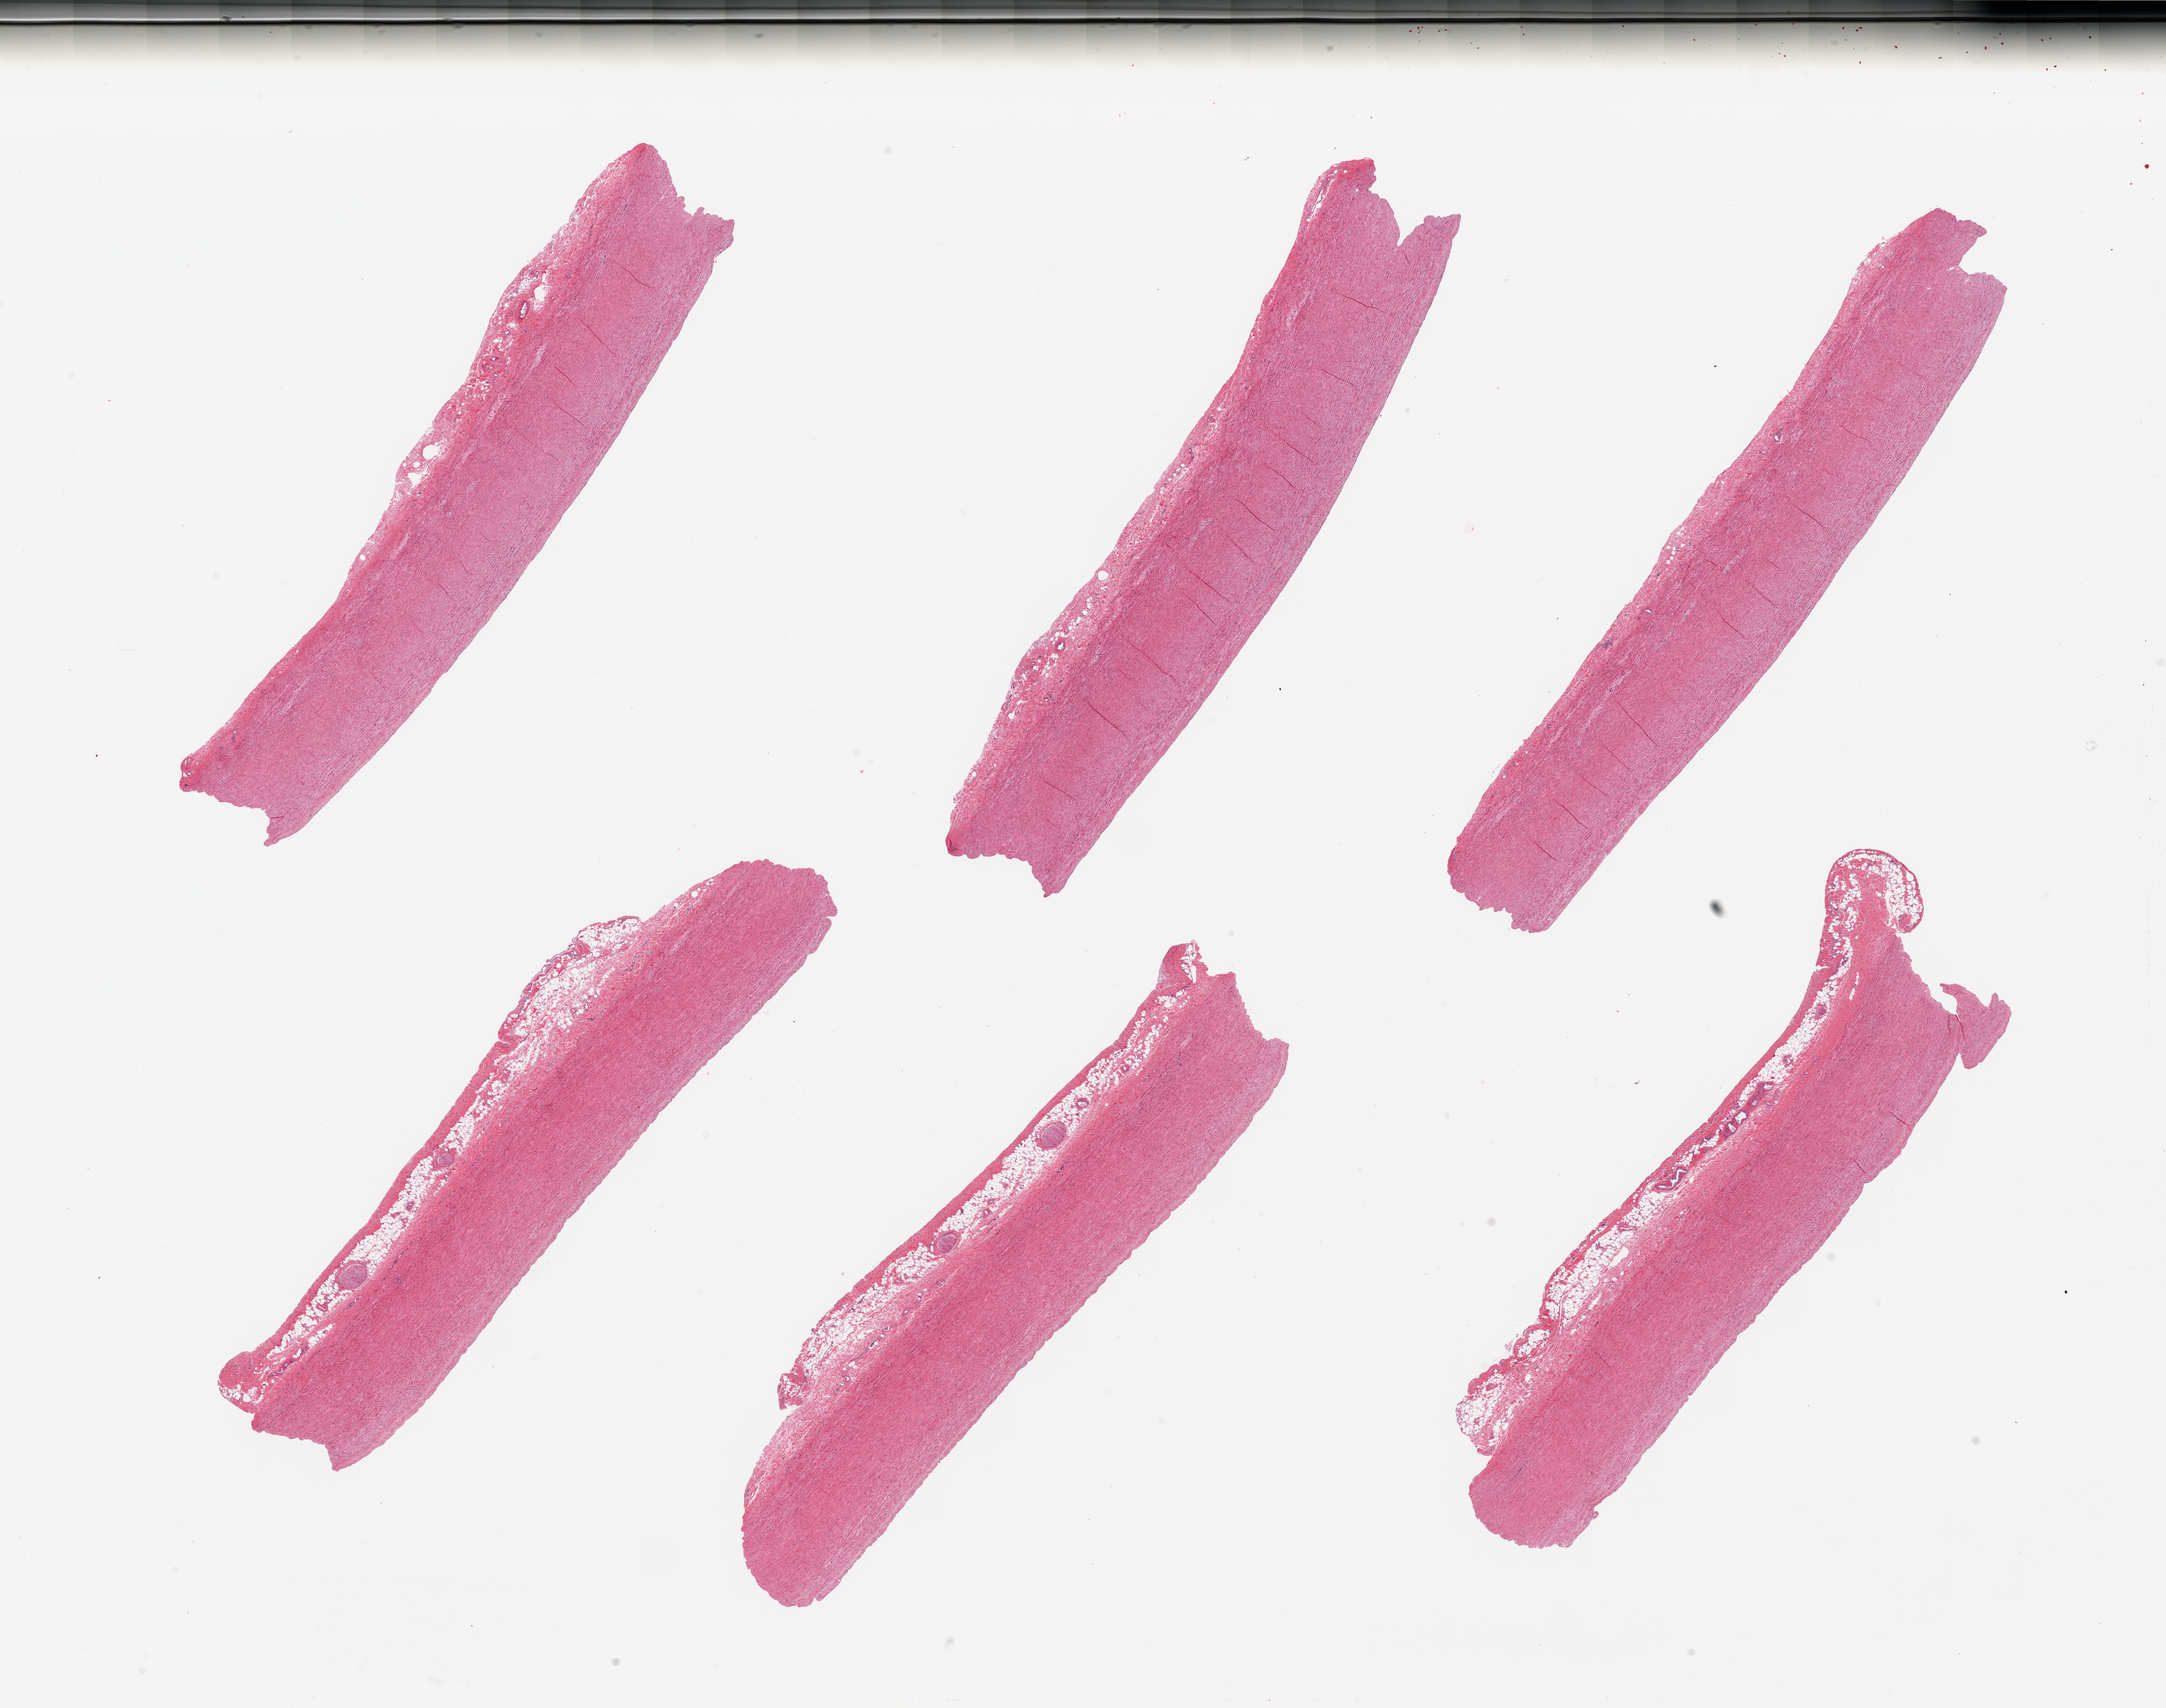
Digitized haematoxylin and eosin-stained section, brightfield, shown as a low-resolution overview of the whole scanned area (about 29.5 x 23.3 mm); PAXgene-fixed, paraffin-embedded tissue; section of aorta (target tissue); donor tissue sample.
Pathologist's review note for this sample: 6 pieces, minimal atherosis, adherent serosa up to ~1mm.